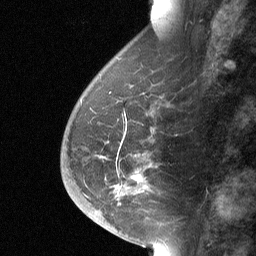
Breast MRI (dynamic contrast-enhanced), one sagittal slice; position 23 of 64 along the scan axis; dynamic contrast-enhanced study with each time point stored as its own series, time point 2 of 3 at this slice position (early post-contrast, ordered by acquisition time); 1.5 T; TE 4.8 ms, TR 27 ms; 256 × 256 image matrix, field of view 180 × 180 mm. Female patient, age 56 years. From the clinical record (not read from this slice): setting: breast cancer imaged before/during neoadjuvant chemotherapy; receptor status: HER2-positive.
Annotated regions visible in this slice (semi-automatic segmentation, software-assisted and operator-edited):
- analysis volume of interest (the breast-tissue region the enhancement analysis was run in; not a lesion): bounding box <68,177,164,214> (left, top, right, bottom; pixels)
- tumour enhancement mask (voxels above the 90 % enhancement threshold inside the analysis volume of interest): <134,177,137,179>